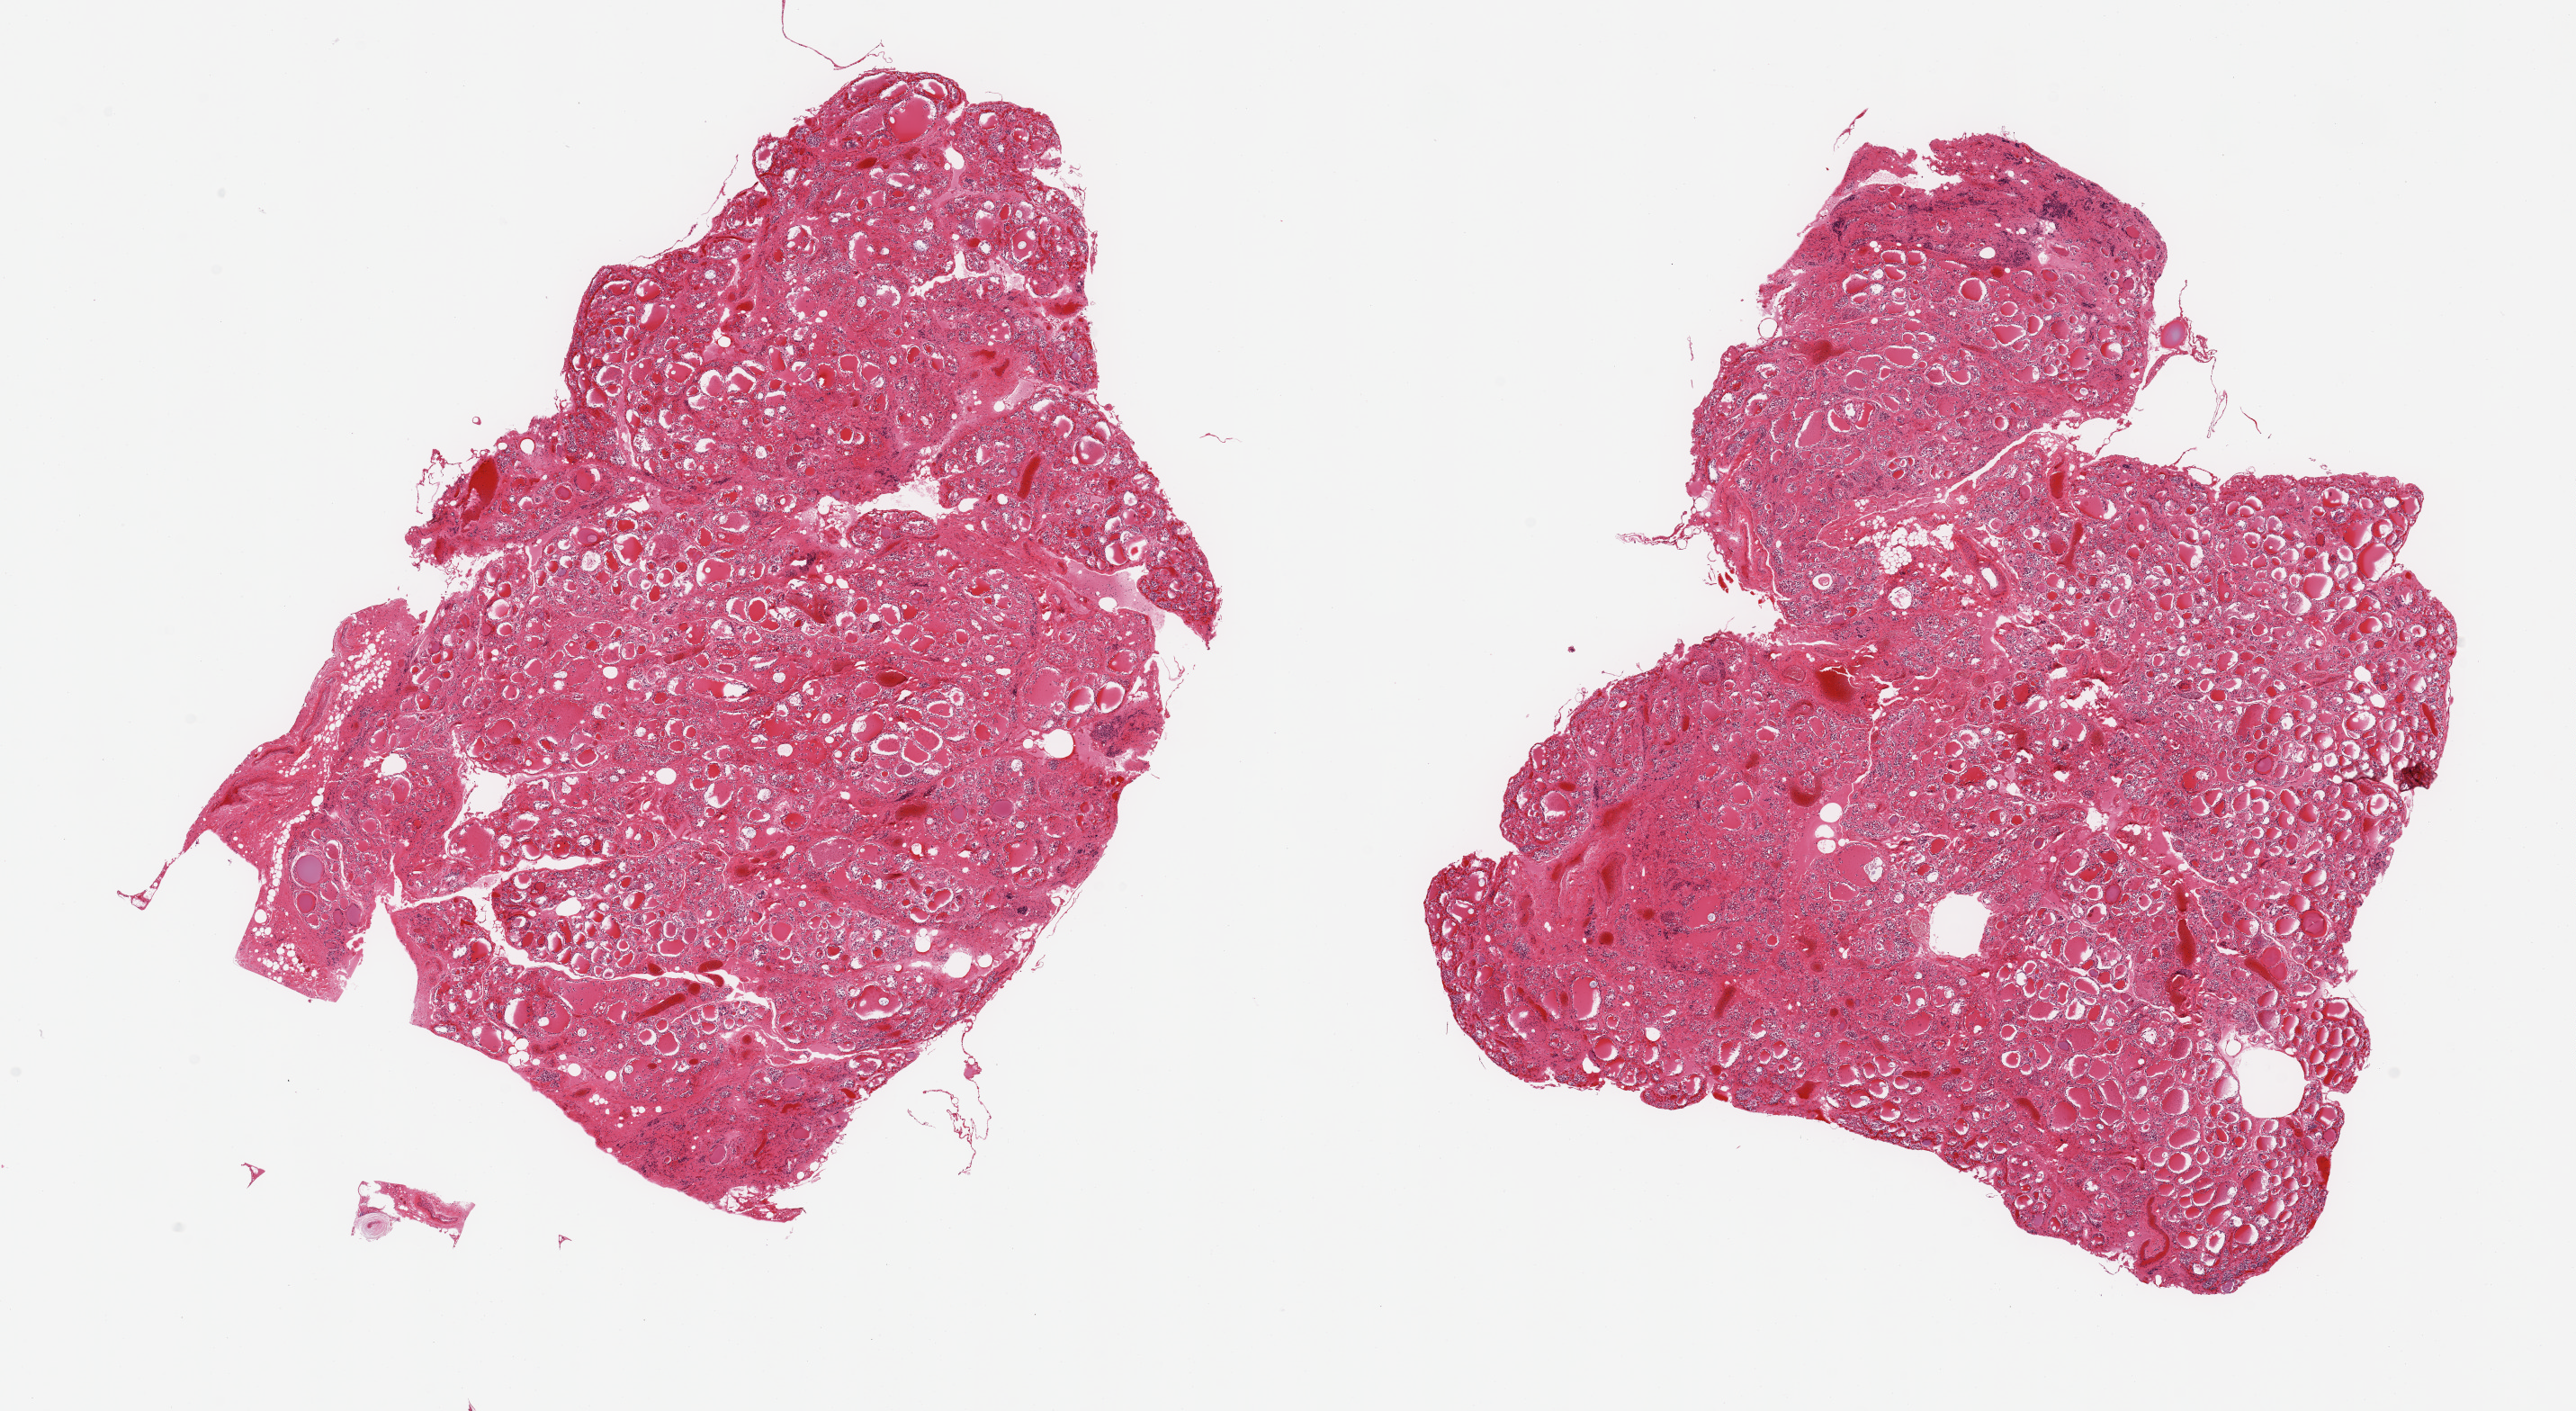
Whole-slide image, hematoxylin and eosin (H&E) stain, a low-resolution overview of the entire scanned area, about 22.6 x 12.4 mm (slide scanned at 20x); PAXgene-fixed, paraffin-embedded tissue; sampled site (target tissue): thyroid; donor tissue sample. Donor sex: male.
Review note (as recorded): 2 pieces, no abnormality, moderately advanced autolysis.